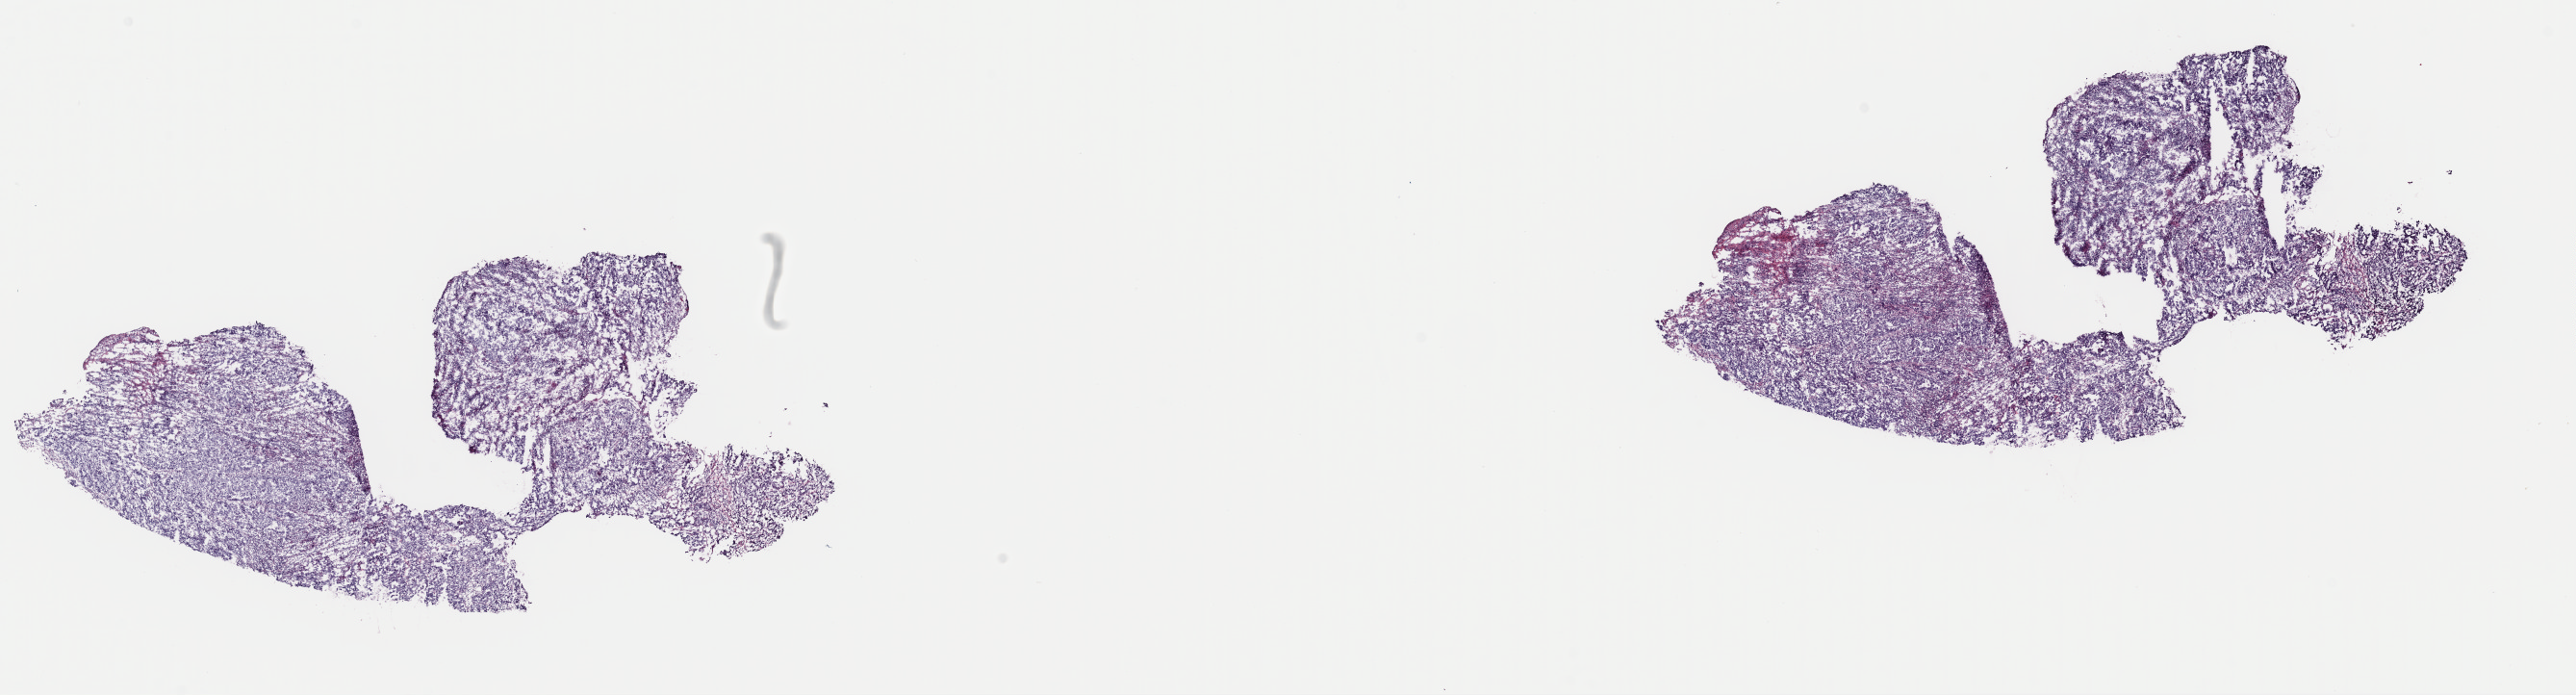
Digitized H&E tissue section (whole slide), whole scanned area (about 21.1 x 5.7 mm, acquisition: 40x scan) shown as a low-resolution overview, frozen section from the top of the tissue portion, sample: primary tumour, stomach. Female patient; age at initial diagnosis 79 years. Histologic grade: G3 (poorly differentiated). Composition of this section per pathologist review: tumour cells 60%, tumour nuclei 70%, normal cells 20%, stromal cells 10%, necrosis 10%. Infiltration values recorded for this section: lymphocyte infiltration 50%, monocyte infiltration 20%, neutrophil infiltration 10%.
AJCC pathologic stage: IB. Histologic diagnosis: Adenocarcinoma, intestinal type (cardia, NOS).